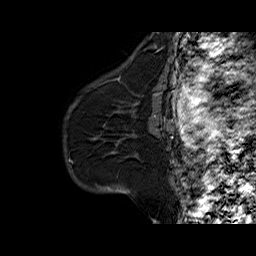
Breast MRI (dynamic contrast-enhanced), one sagittal slice. Slice 45 of 60 in the series (ordered by position). Dynamic contrast-enhanced series, time point 2 of 6 at this slice position (early post-contrast). 1.5 T. TE 6.3 ms, TR 32.5 ms. 4 mm slice thickness. 256 × 256 image matrix, field of view 200 × 200 mm. Female patient. From the clinical record (not read from this slice): setting: breast cancer imaged before/during neoadjuvant chemotherapy; receptor status: HR-positive, HER2-negative.
Structures marked on this image (semi-automatically segmented with operator editing):
- analysis volume of interest (the breast-tissue region the enhancement analysis was run in; not a lesion): box from (x=94, y=103) to (x=161, y=158) px
- tumour enhancement mask (voxels above the 100 % enhancement threshold inside the analysis volume of interest): (x=154, y=115)–(x=156, y=117)